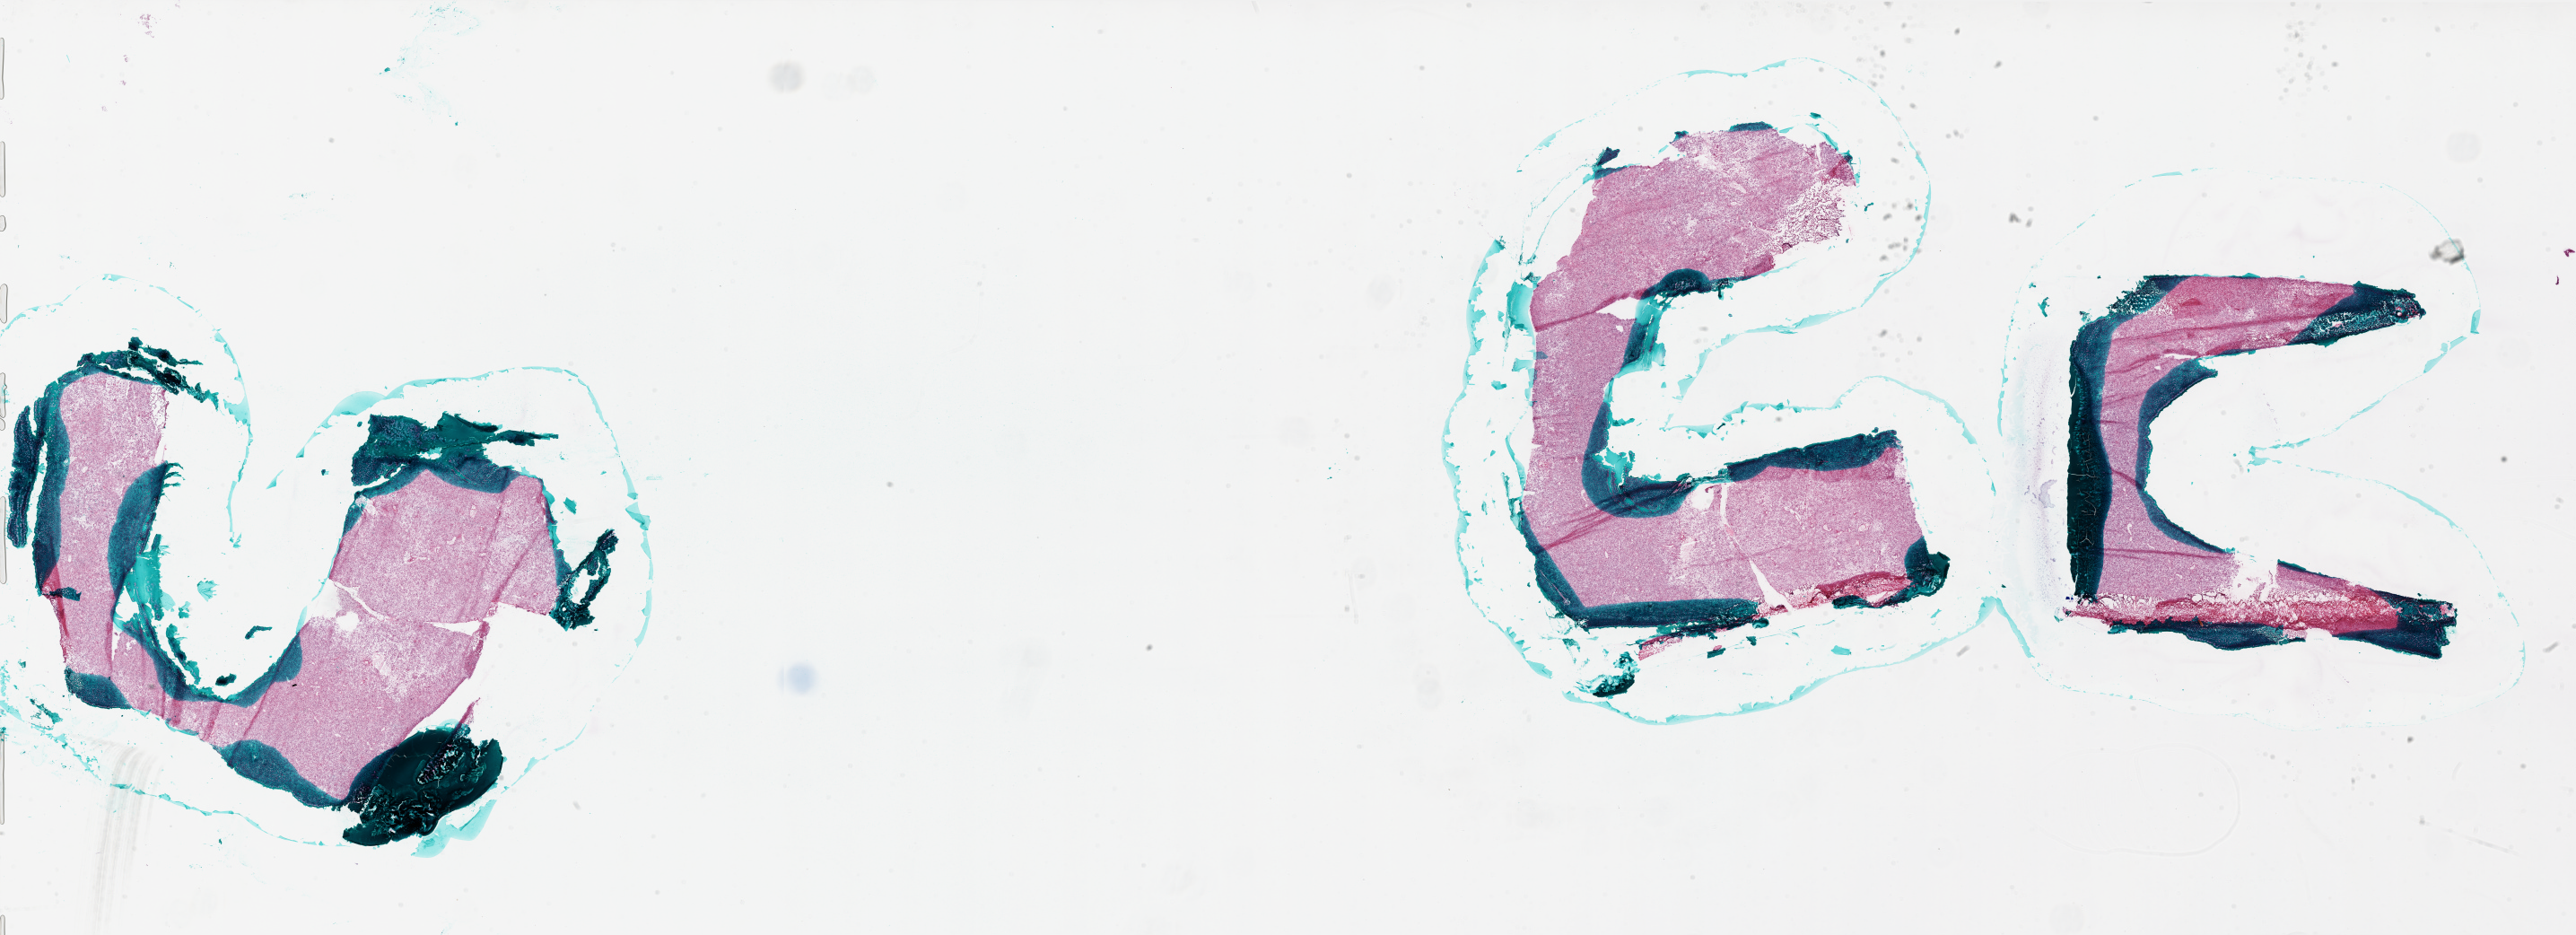
Whole-slide histology image, Hematoxylin and eosin (H&E) stained — whole scanned area (about 46.0 x 16.7 mm) shown as a low-resolution overview. Frozen section from the bottom of the tissue portion. Brain, primary tumour sample. Patient: male, age at initial diagnosis 61 years. Slide review estimates, as recorded: tumour cells 90%, tumour nuclei 100%, normal cells 0%, stromal cells 0%, necrosis 10%.
Pathologic diagnosis: Glioblastoma.